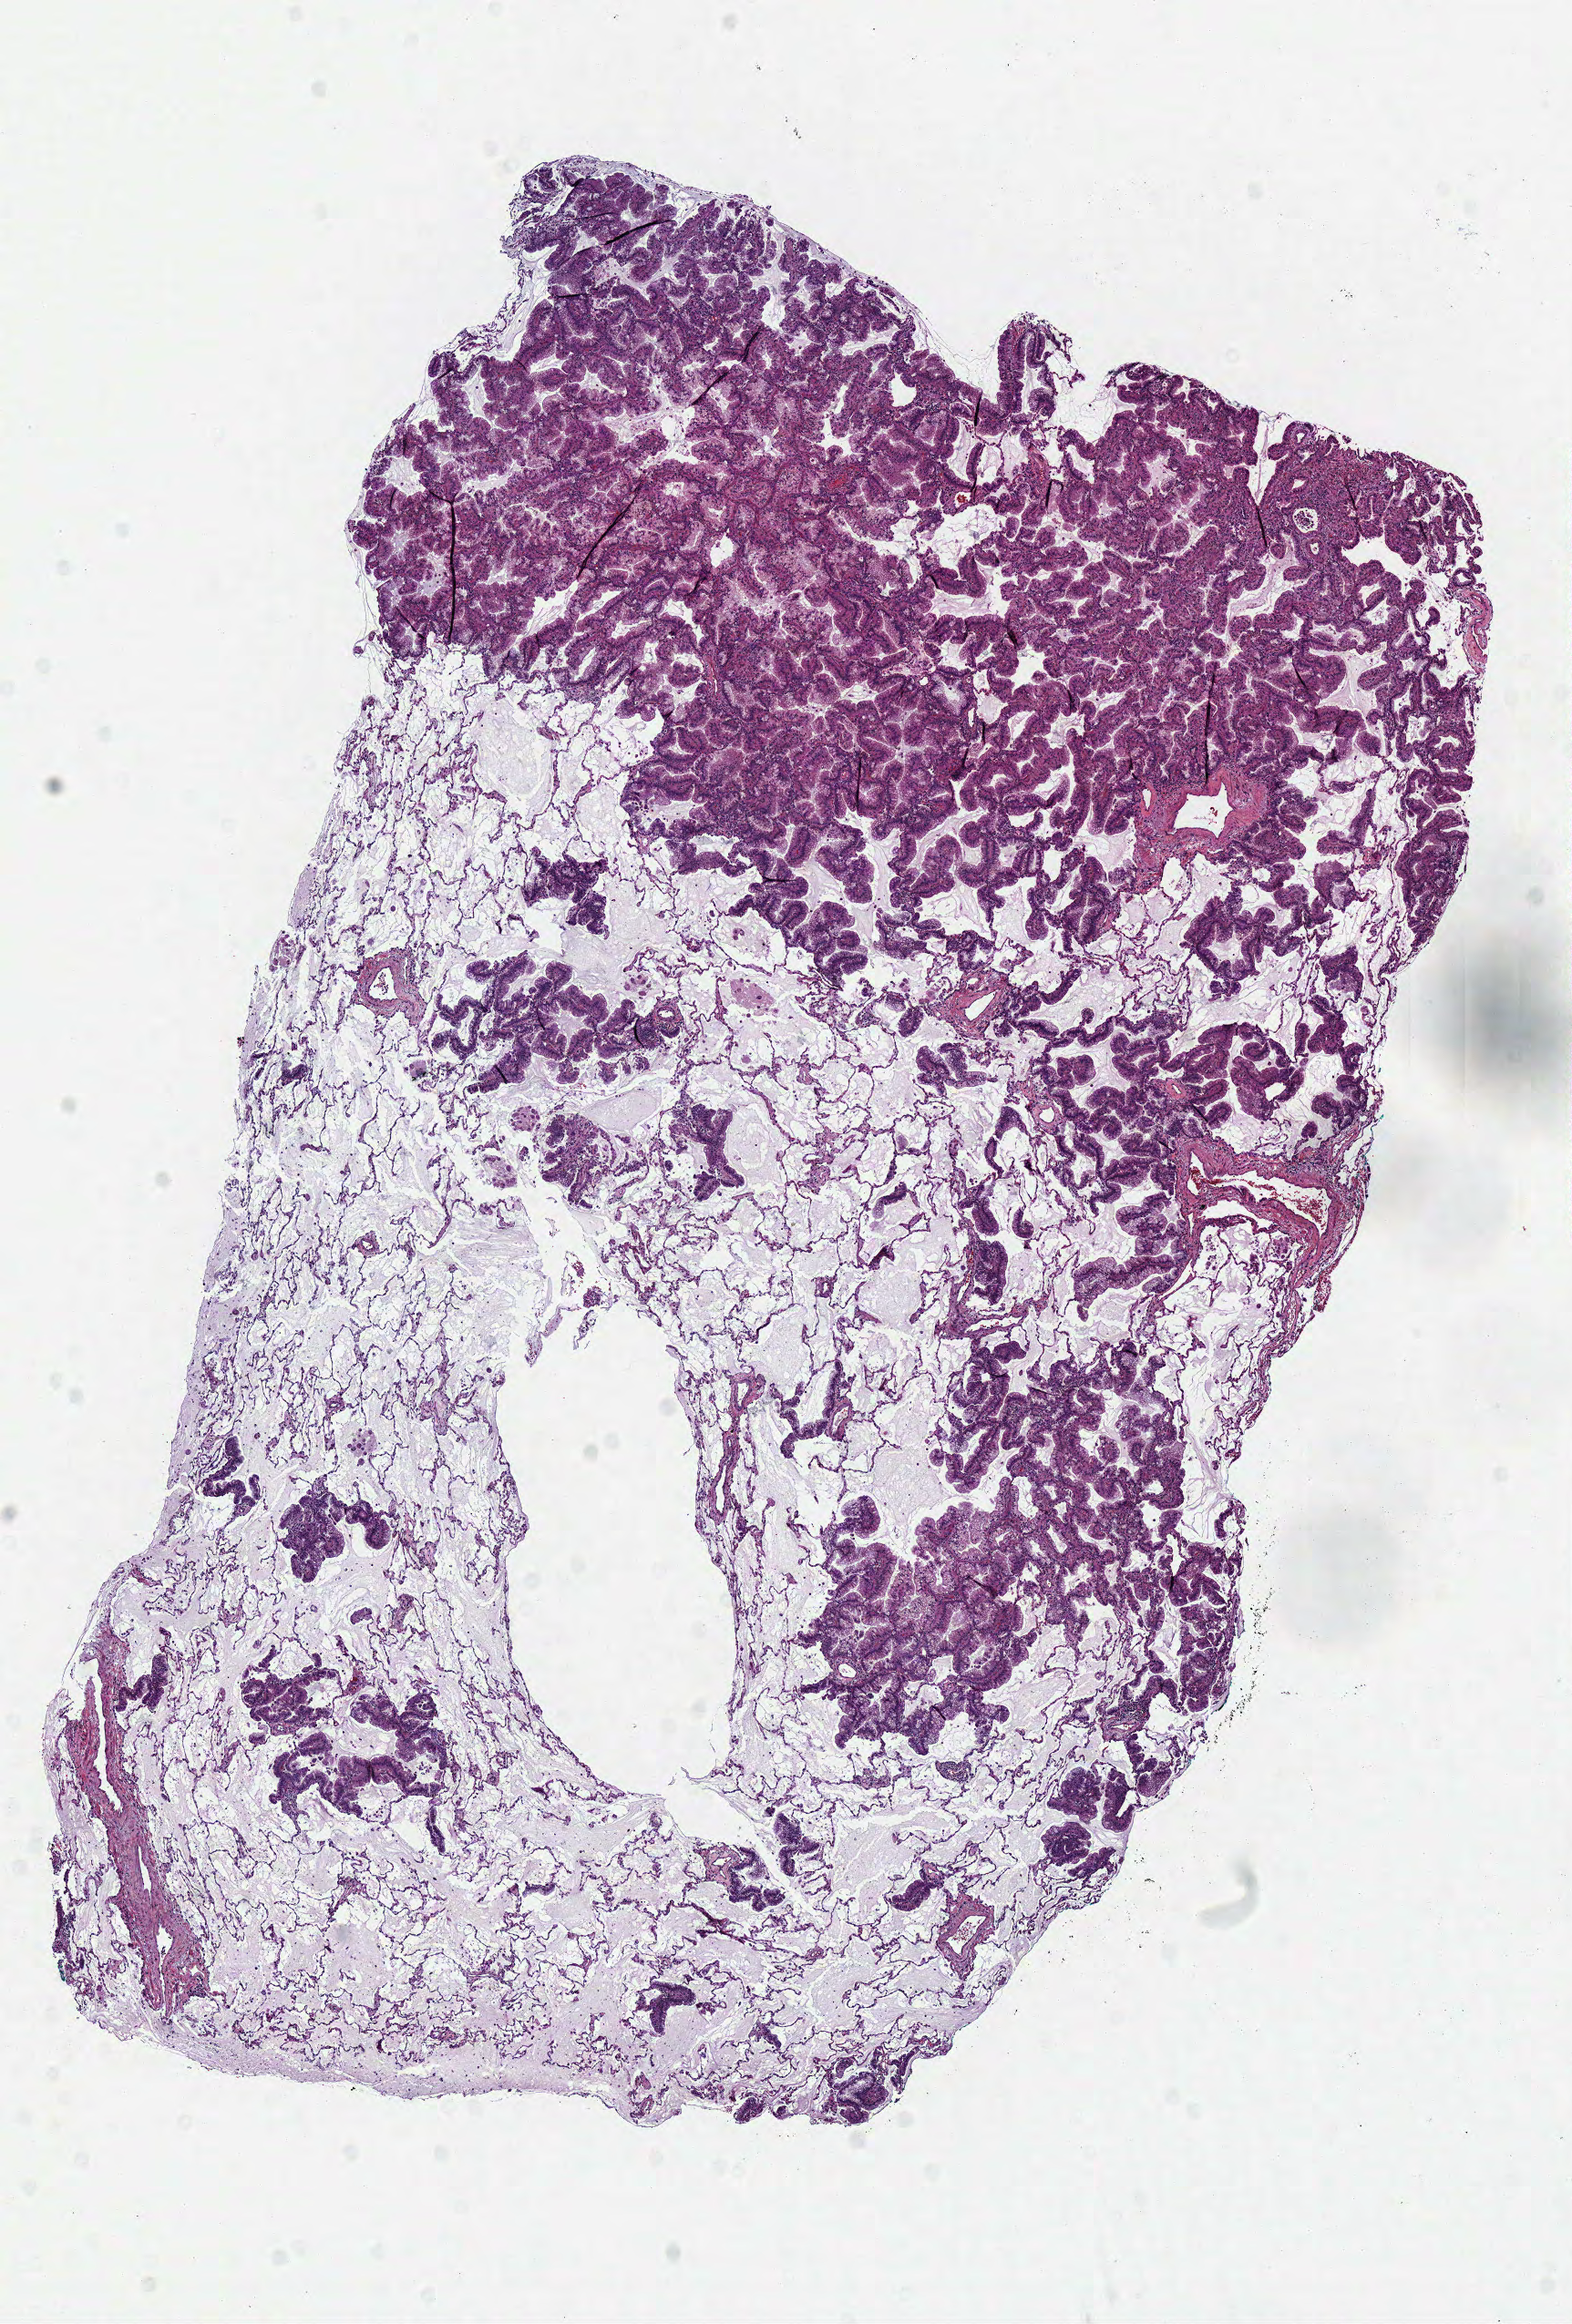
Digitized H&E tissue section (whole slide) — low-resolution overview of the scanned area, about 6.8 x 10.1 mm (from a 40x scan). Frozen section. Primary tumour sample from the lung. Male, age 64 years at initial diagnosis. Pathologist review of this section (percent, as recorded): tumour cells 90%, tumour nuclei 90%, normal cells 10%, stromal cells 0%, necrosis 0%. Inflammatory infiltration, as recorded: lymphocyte infiltration 2%, monocyte infiltration 2%, neutrophil infiltration 0%.
Diagnosis: Mucinous adenocarcinoma (lower lobe, lung). AJCC pathologic stage: IIB (7th edition). Laterality: left.